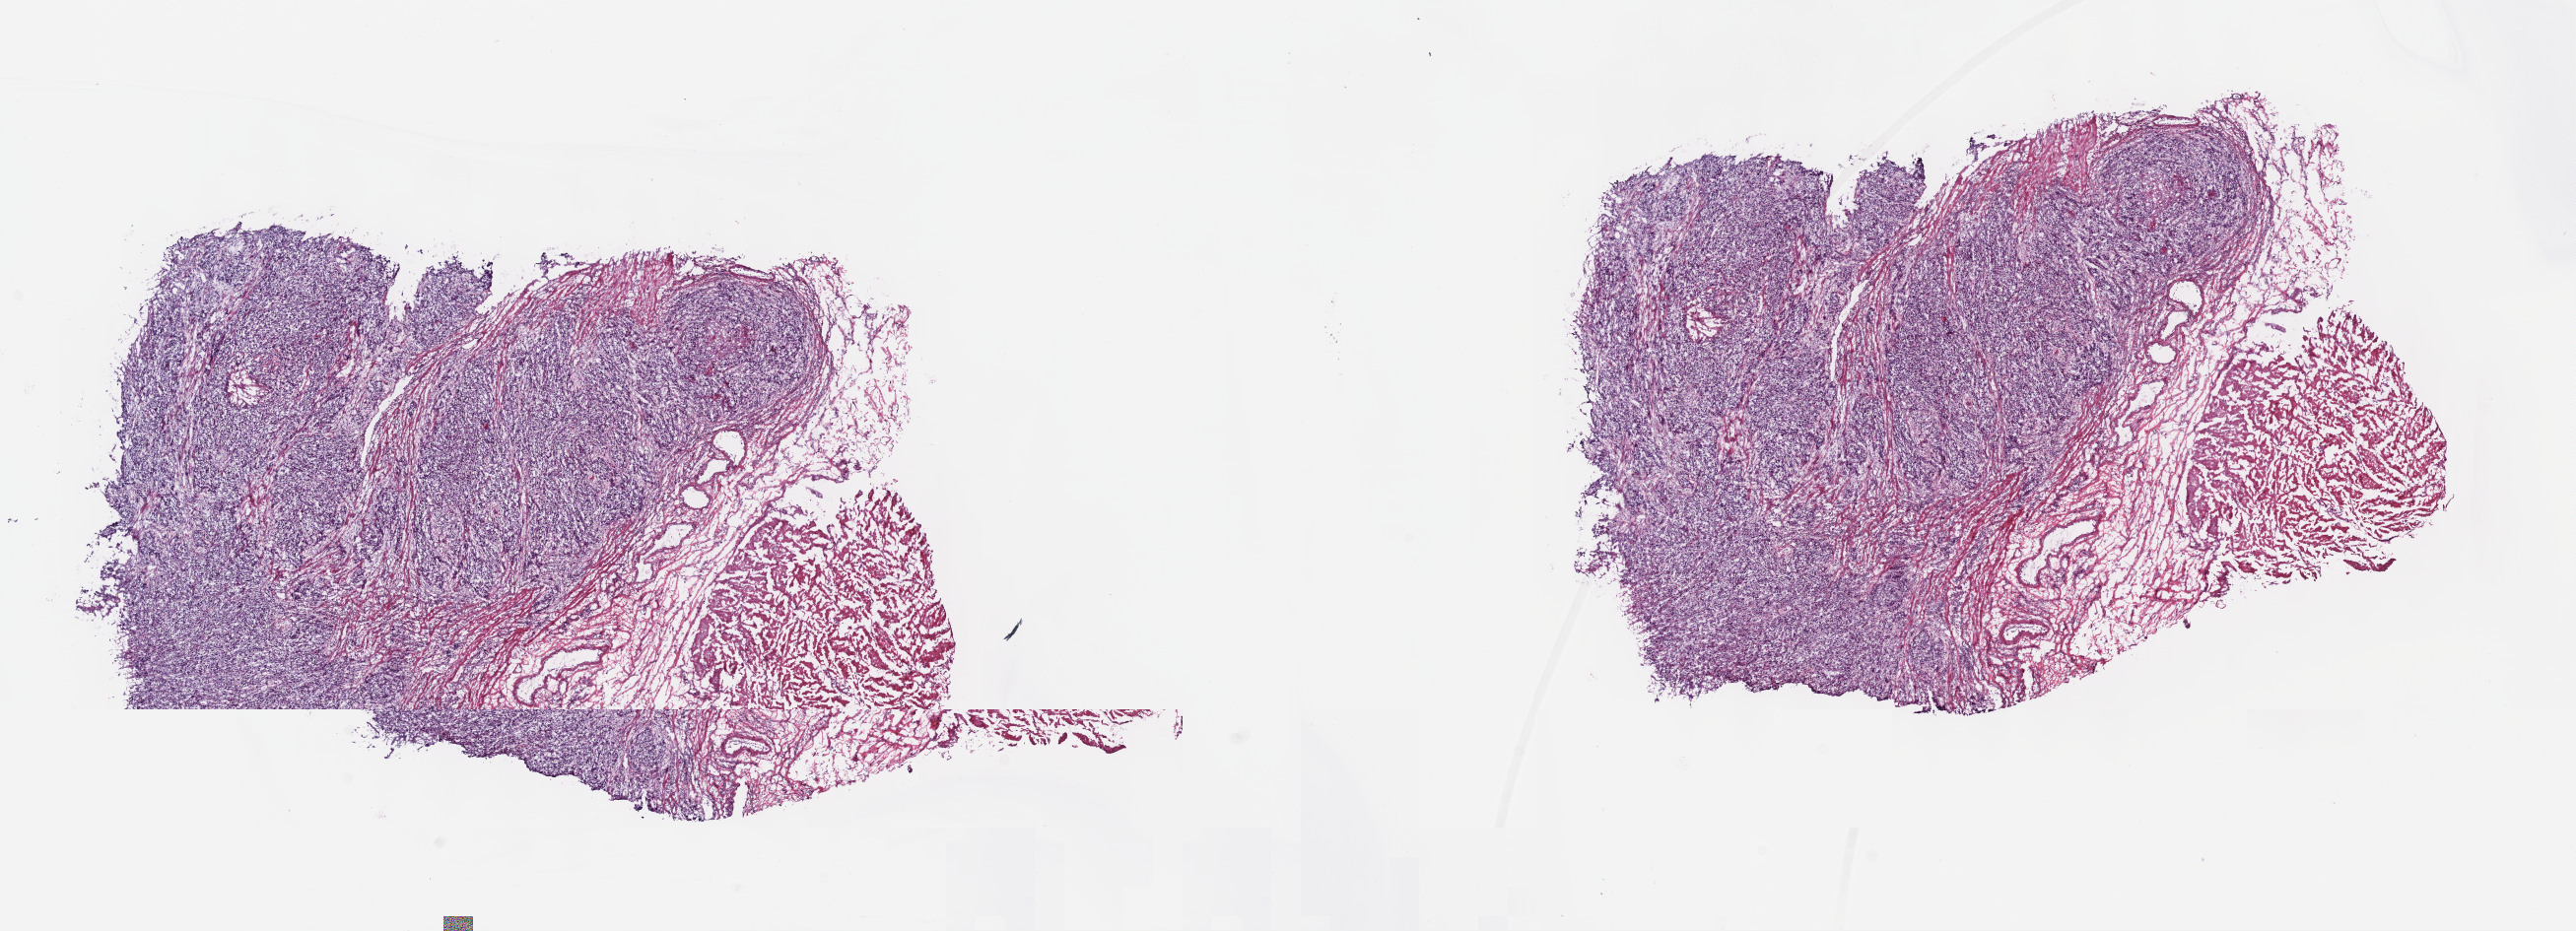
H&E-stained whole-slide image, whole scanned area (about 21.1 x 7.6 mm) shown as a low-resolution overview, frozen section, sample: primary tumour, esophagus. Male, age 84 years at initial diagnosis. Histologic grade: GX (grade cannot be assessed). Pathologist review of this section (percent, as recorded): tumour cells 70%, tumour nuclei 75%, normal cells 30%, stromal cells 0%, necrosis 0%. Infiltration values recorded for this section: lymphocyte infiltration 2%, monocyte infiltration 0%, neutrophil infiltration 0%.
Lymph nodes positive (case pathology): 0 of 8 examined. Diagnosis: Squamous cell carcinoma, NOS (lower third of esophagus). AJCC pathologic stage: IB (7th edition).